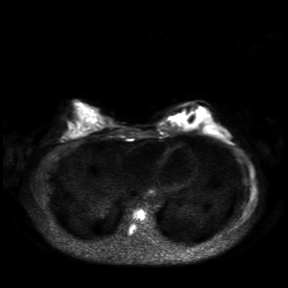
Breast MRI, one axial slice. Position 11 of 30 along the scan axis. Diffusion-weighted series; image 2 of 4 stored at this slice position (different b-values; order by instance number). 3 T. 4 mm slice thickness. 288 × 288 image matrix, field of view 360 × 360 mm. Female patient.
Structures marked on this image (expert manual segmentation):
- tumour on diffusion-weighted imaging: bounding box <170,116,178,123> (left, top, right, bottom; pixels)